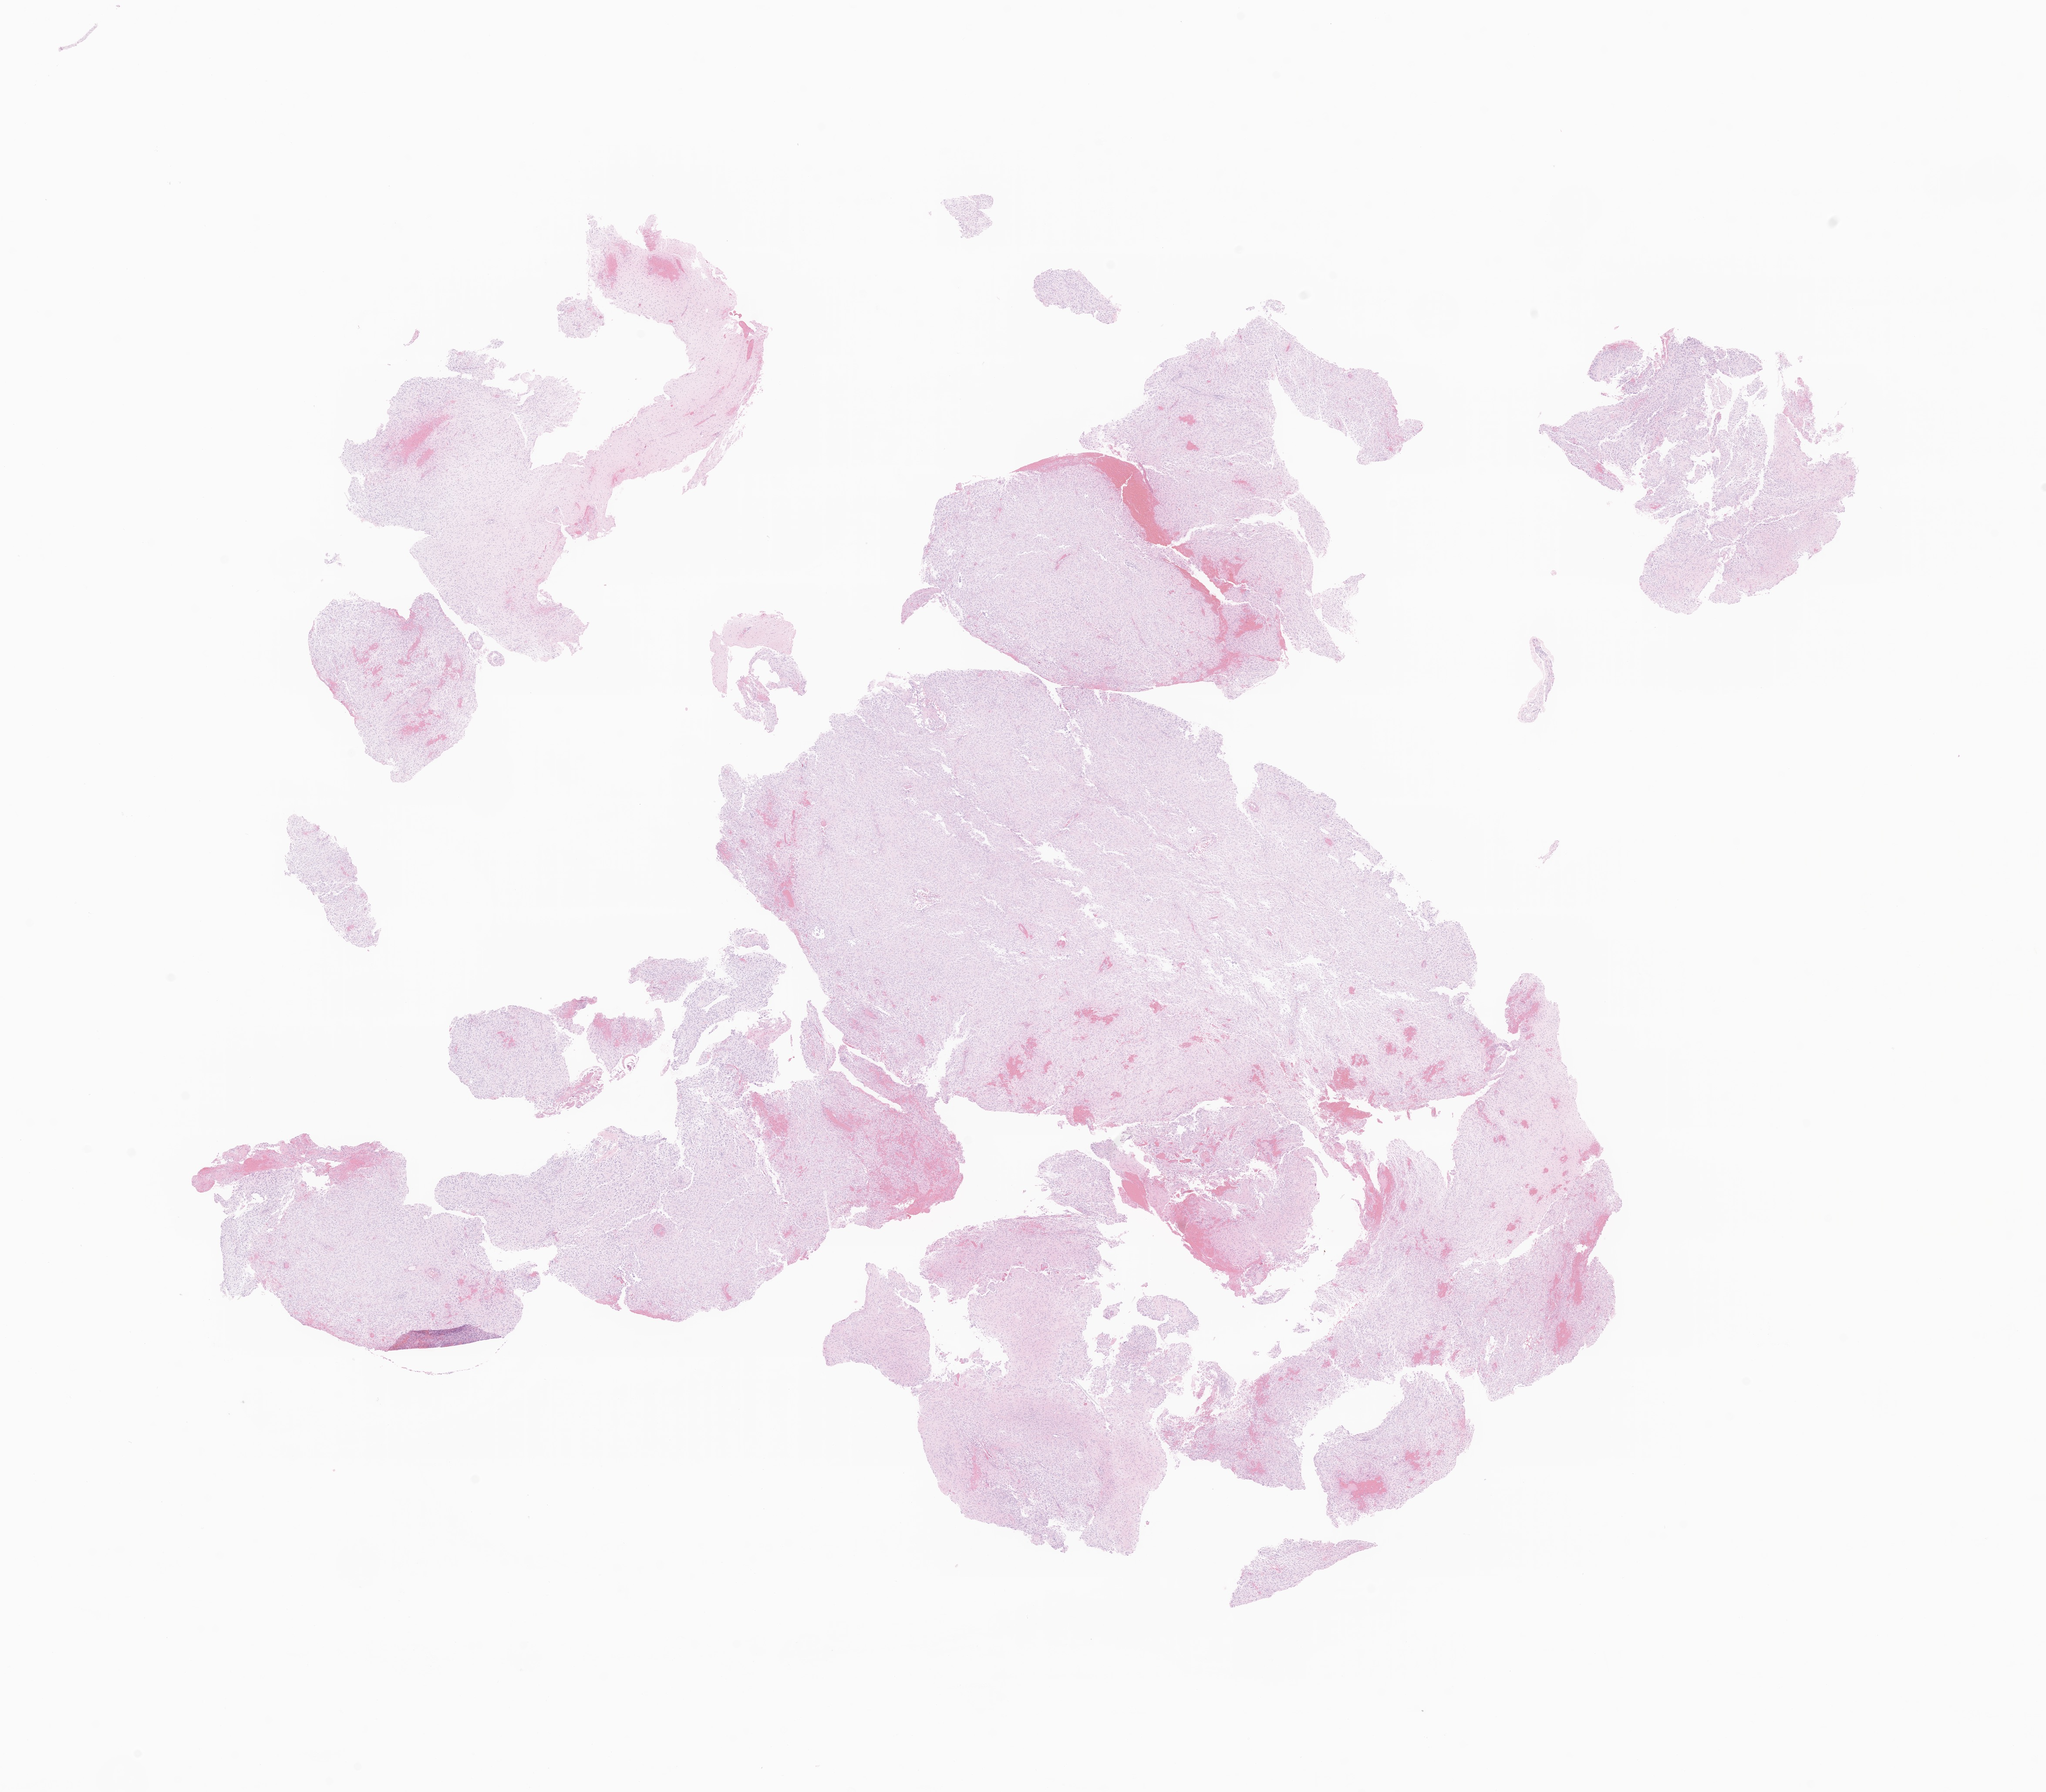
Digitized haematoxylin and eosin-stained section of tumor tissue from the brain, whole scanned area (about 19.8 x 17.4 mm) shown as a low-resolution overview, formalin-fixed paraffin-embedded section. Patient male; age 150 months (12 years 6 months).
* recorded diagnosis: Pilocytic astrocytoma